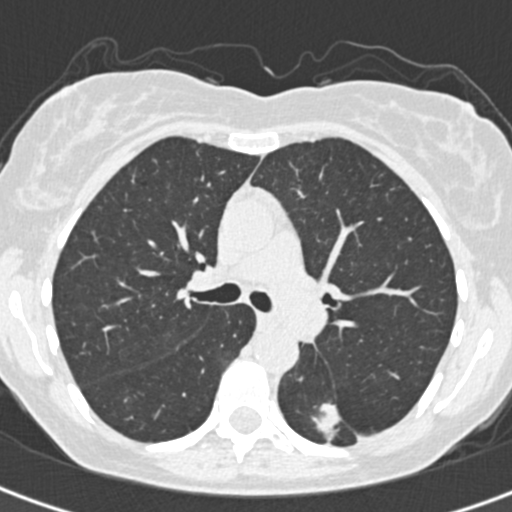
Low-dose screening chest CT, one axial slice. Slice 211 of 328 in the series (ordered by position). Lung window (W 1500 / L -600 HU). 512 × 512 image matrix, field of view 284 × 284 mm.
Outlined on this slice (manually delineated by an expert):
- lesion 1 (tumor, lower lobe of left lung): box from (x=315, y=402) to (x=341, y=439) px